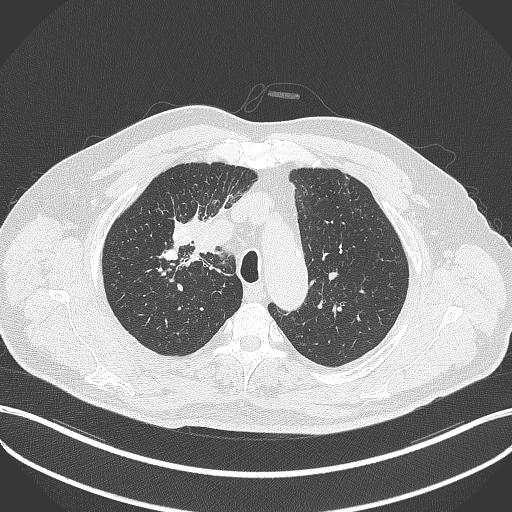
Chest CT, one axial slice. Position 304 of 411 along the scan axis. Reconstruction kernel B70f. Lung window (W 1500 / L -600 HU). 1 mm slice thickness. 512 × 512 image matrix. Male patient, age 60 years. Case-level facts recorded for this patient, not image findings: clinical TNM (as recorded): T1b N1 M0.
Annotated regions visible in this slice (rectangle marked by the reading radiologist):
- lung tumour (recorded histology: squamous cell carcinoma): bounding box (x1, y1, x2, y2) in pixels: (188, 228, 219, 261)